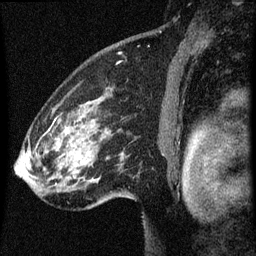
Breast MRI (dynamic contrast-enhanced), one sagittal slice; slice 47 of 60 in the series (ordered by position); dynamic contrast-enhanced series, image 2 of 3 at this slice position (ordered by acquisition); 1.5 T; TE 4.2 ms, TR 8 ms; 2 mm slice thickness; 256 × 256 image matrix, field of view 180 × 180 mm. Female patient, age 61 years.
Outlined on this slice (semi-automatically segmented with operator editing):
- analysis volume of interest (the breast-tissue region the enhancement analysis was run in; not a lesion): bounding box (x1, y1, x2, y2) in pixels: (27, 86, 134, 209)
- tumour enhancement mask (voxels above the 70 % enhancement threshold inside the analysis volume of interest): (36, 130, 65, 149)